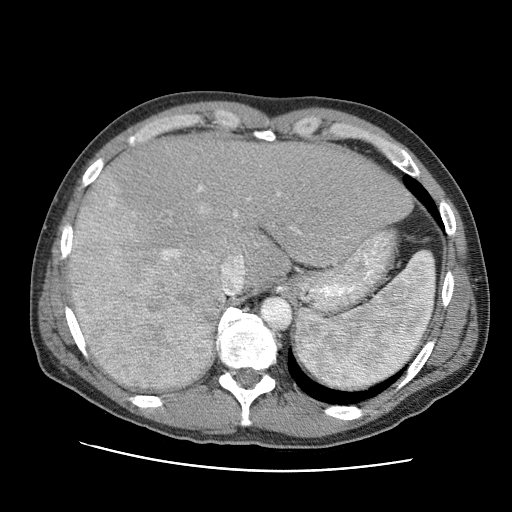
Contrast-enhanced abdominal CT (liver protocol), one axial slice. Slice 70 of 95 in the series (ordered by position). Reconstruction kernel STANDARD. One of 2 acquisitions stored at this slice position. Soft-tissue window (W 400 / L 40 HU). 2.5 mm slice thickness. 512 × 512 image matrix, field of view 360 × 360 mm. Case-level facts recorded for this patient, not image findings: diagnosis: hepatocellular carcinoma (patient treated with transarterial chemoembolisation; whether this scan precedes or follows treatment is not stated here); TNM stage (as recorded): Stage-IVA; Child-Pugh class: A; tumour differentiation: moderately differentiated; tumour nodularity: multinodular.
Annotated regions visible in this slice (semi-automatically segmented with operator editing):
- liver parenchyma outside the tumour (the mass and vessels are separate outlines, so this box may not span the whole liver): bounding box [x1, y1, x2, y2] px = [68, 136, 412, 390]
- mass: [68, 171, 224, 390]
- liver vessels: [86, 185, 301, 338]